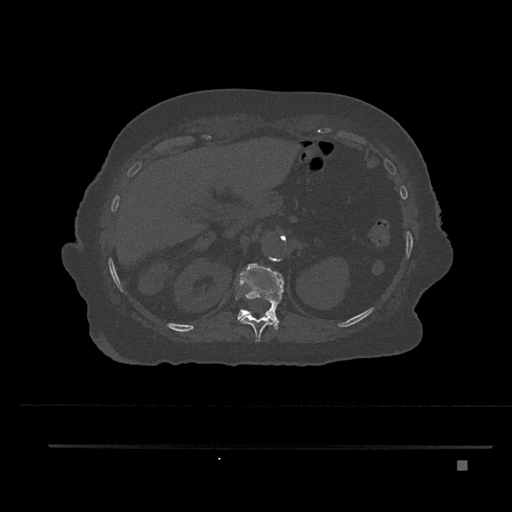
CT including the spine, one axial slice; slice 289 of 797 in the series (ordered by position); reconstruction kernel Br40s/3; 120 kVp; bone window (W 1800 / L 400 HU); 0.5 mm slice thickness; 512 × 512 image matrix. Patient: female, 76 years. Case-level facts recorded for this patient, not image findings: primary cancer: lung; vertebrae with lytic lesions (as recorded): T11, L3.
Annotated regions visible in this slice (semi-automatic segmentation, software-assisted and operator-edited):
- T11 vertebra: box from (x=239, y=314) to (x=277, y=342) px
- T12 vertebra: (x=235, y=263)–(x=284, y=330)